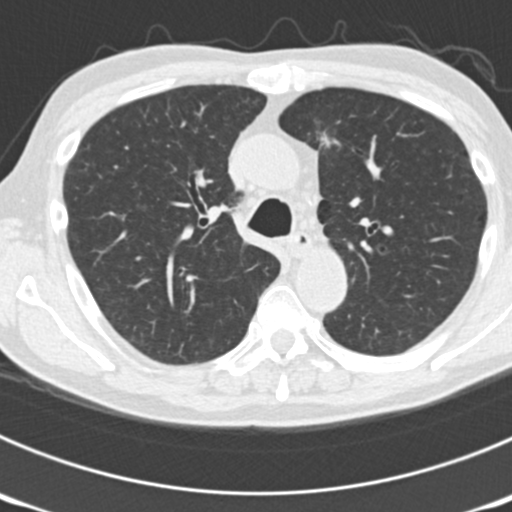
Low-dose screening chest CT, one axial slice; position 127 of 177 along the scan axis; reconstruction kernel B30f; 120 kVp; lung window (W 1500 / L -600 HU); 2 mm slice thickness; 512 × 512 image matrix.
Outlined on this slice (outlined manually by an expert reader):
- lesion 4 (tumor): bounding box <316,130,332,148> (left, top, right, bottom; pixels)